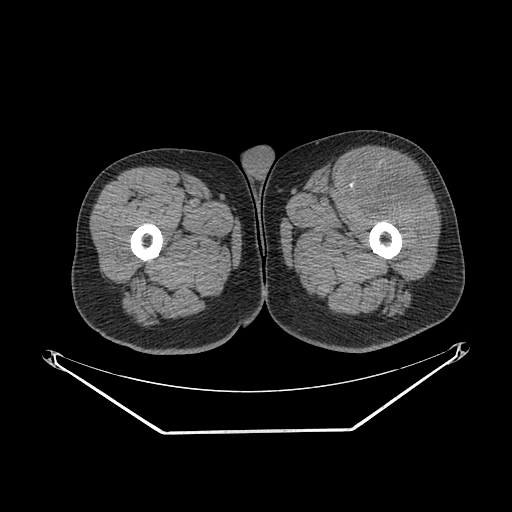
CT of an extremity soft-tissue mass (from a PET/CT study), one axial slice; slice 246 of 267 in the series (ordered by position); 140 kVp; soft-tissue window (W 400 / L 40 HU); 3.75 mm slice thickness; 512 × 512 image matrix, field of view 500 × 500 mm. Male patient. Case-level facts recorded for this patient, not image findings: histological type: extraskeletal osteosarcoma; grade: high; site of the primary tumour: thigh.
Outlined on this slice (expert contour drawn on MRI and transferred to this co-registered scan by the dataset authors):
- gross tumour volume (mass): bounding box <354,162,426,209> (left, top, right, bottom; pixels)